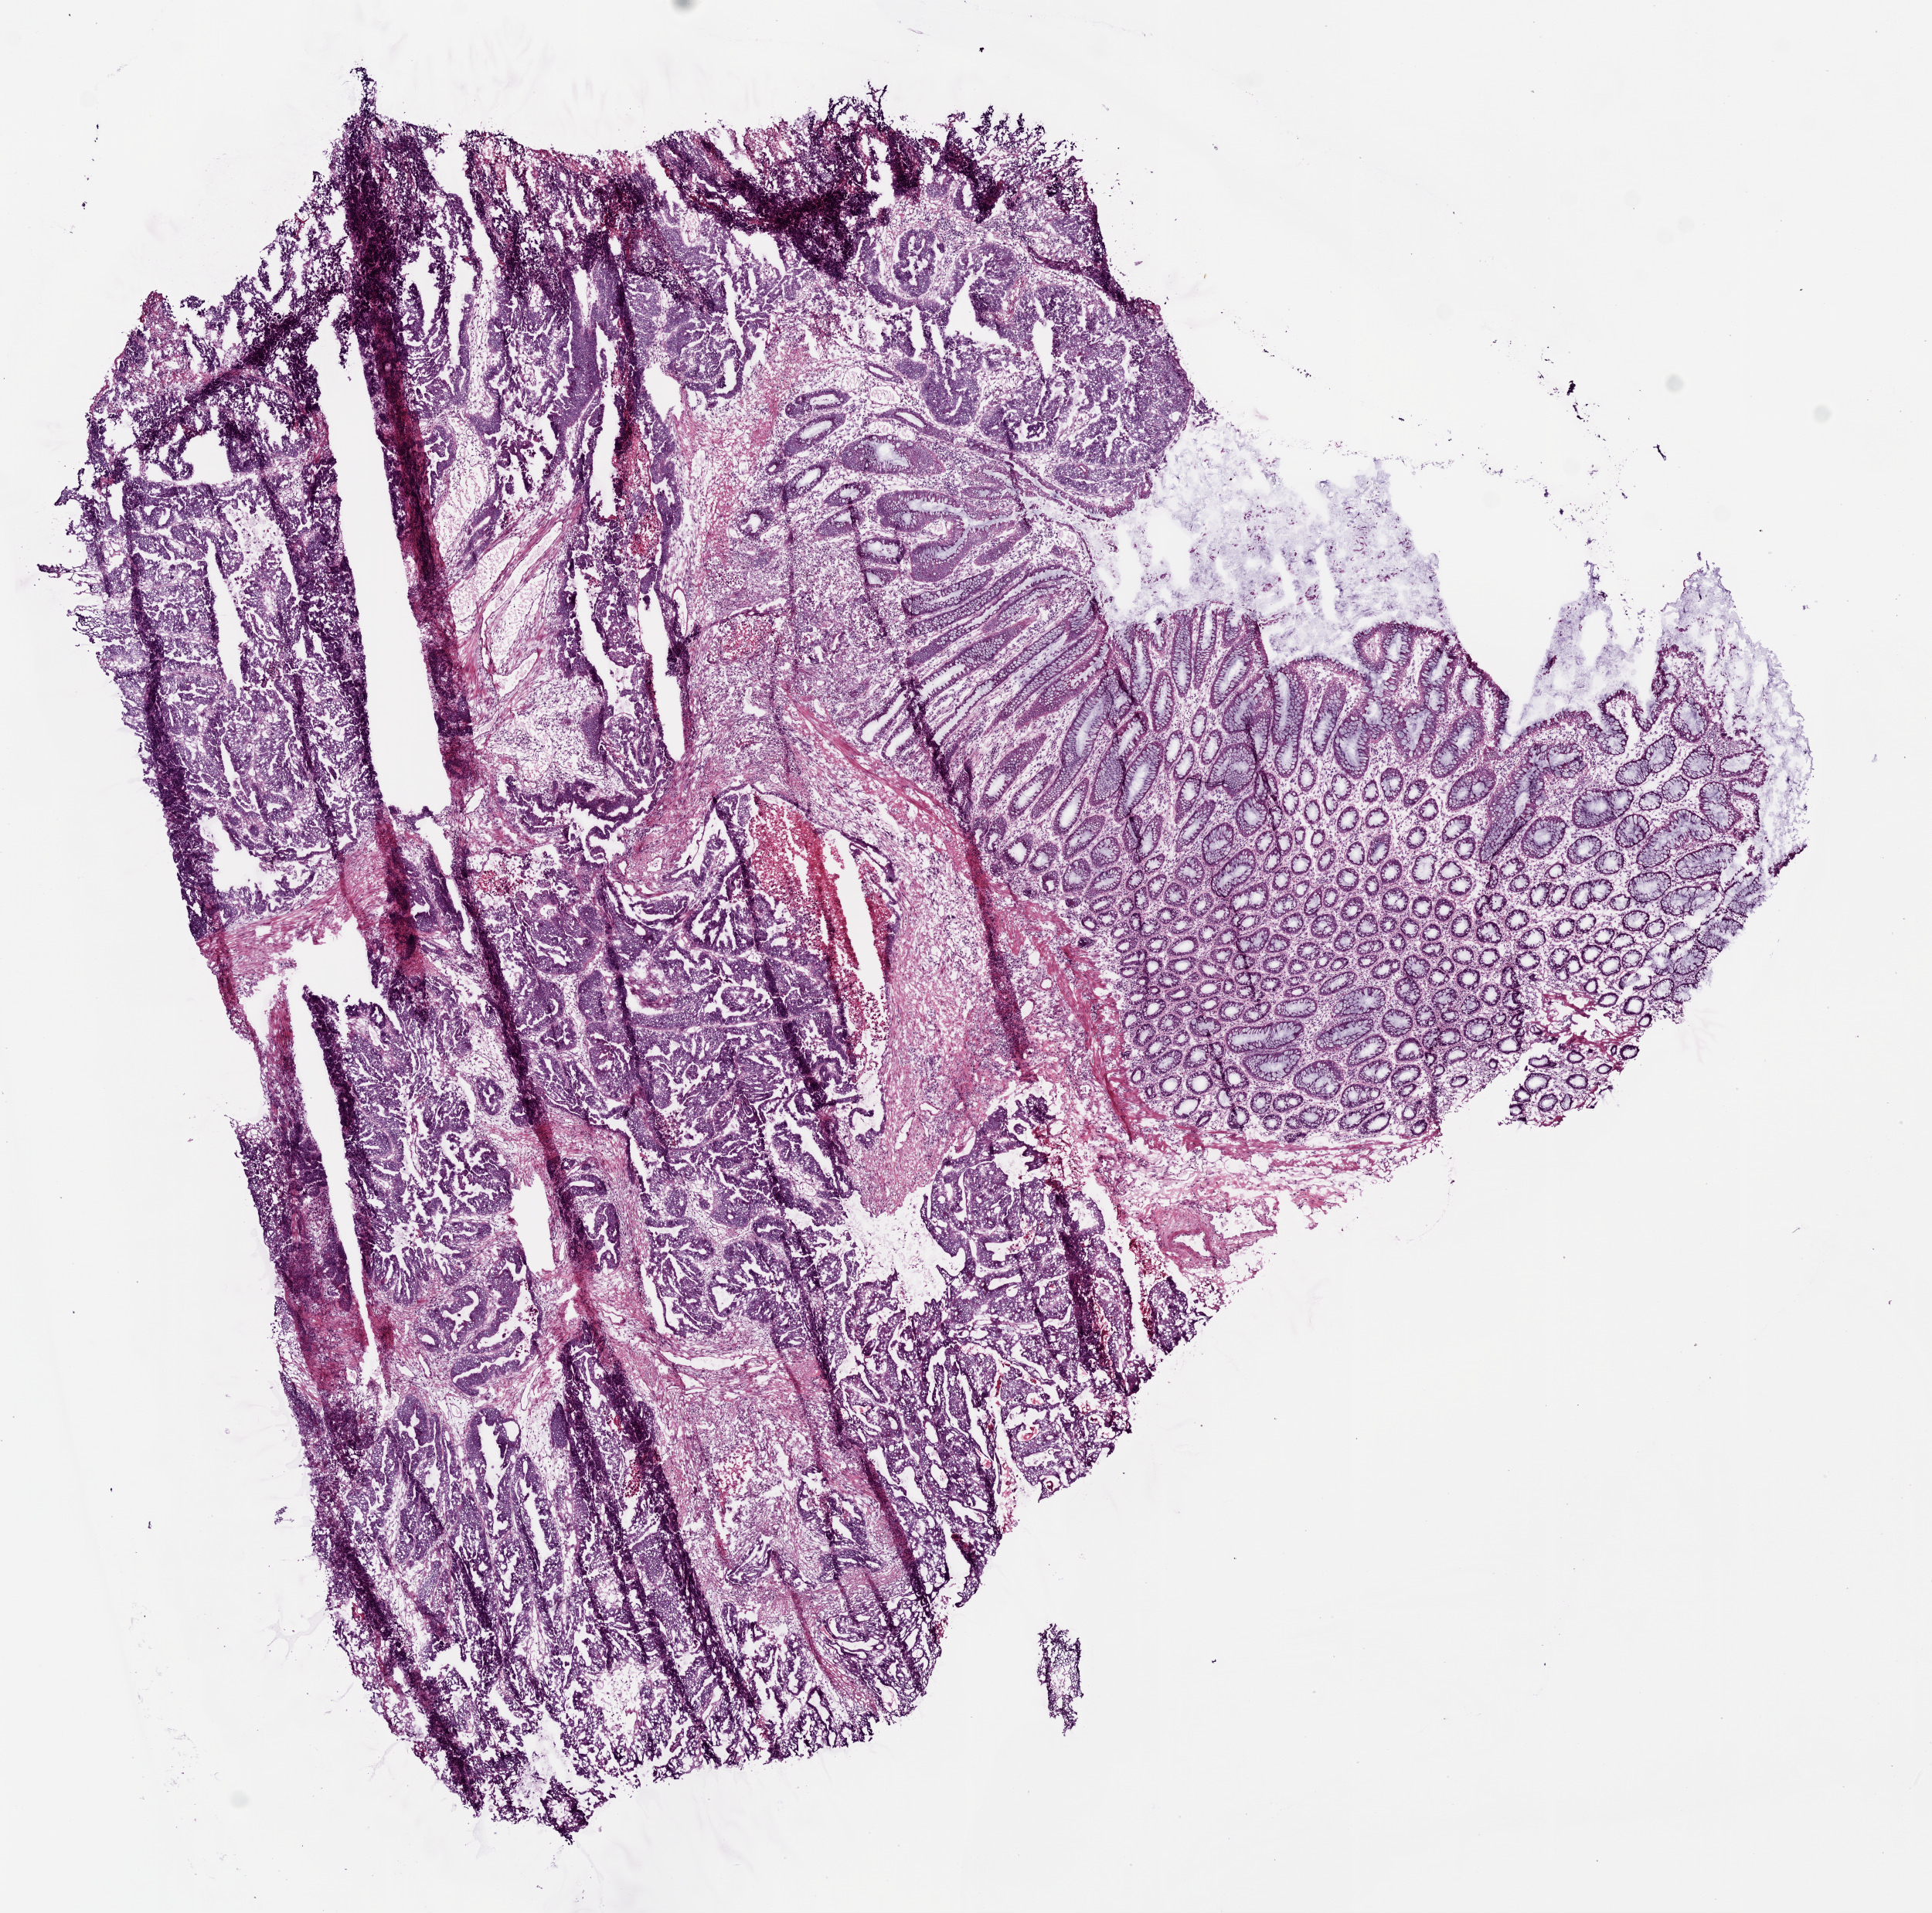
H&E-stained whole-slide image — a low-resolution overview of the entire scanned area, about 10.0 x 9.9 mm; frozen section from the bottom of the tissue portion; colon, primary tumour sample. Male patient; age at initial diagnosis 61 years. Slide review estimates, as recorded: tumour cells 57%, tumour nuclei 70%.
Pathologic diagnosis: Adenocarcinoma, NOS (rectosigmoid junction).